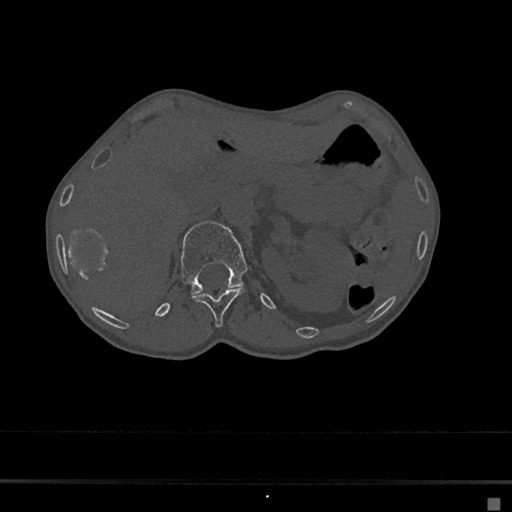
CT including the spine, one axial slice; slice 92 of 797 in the series (ordered by position); reconstruction kernel Br40s/3; 120 kVp; bone window (W 1800 / L 400 HU); 512 × 512 image matrix, field of view 360 × 360 mm. Patient: female, 68 years. Case-level facts recorded for this patient, not image findings: primary cancer: renal.
Structures marked on this image (semi-automatic segmentation, software-assisted and operator-edited):
- L1 vertebra: bounding box (x1, y1, x2, y2) in pixels: (180, 221, 248, 295)
- T12 vertebra: (192, 288, 244, 328)